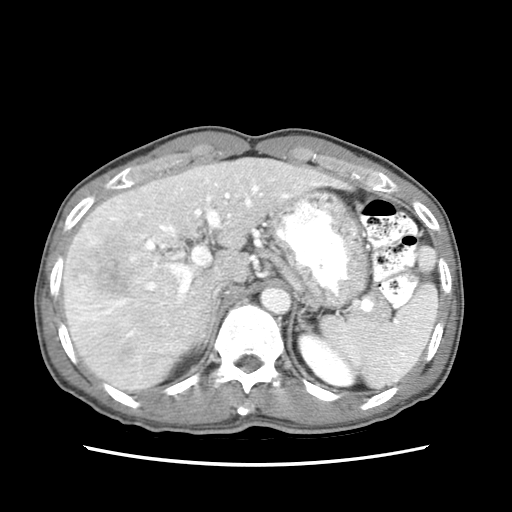
Contrast-enhanced abdominal CT (liver protocol), one axial slice. Position 47 of 79 along the scan axis. Reconstruction kernel STANDARD. Soft-tissue window (W 400 / L 40 HU). 512 × 512 image matrix. Case-level facts recorded for this patient, not image findings: diagnosis: hepatocellular carcinoma (patient treated with transarterial chemoembolisation; whether this scan precedes or follows treatment is not stated here); TNM stage (as recorded): Stage-IIIB; Child-Pugh class: A; tumour differentiation: moderately differentiated; tumour nodularity: multinodular.
Annotated regions visible in this slice (semi-automatically segmented with operator editing):
- liver parenchyma outside the tumour (the mass and vessels are separate outlines, so this box may not span the whole liver): bounding box <62,156,366,391> (left, top, right, bottom; pixels)
- mass: <63,197,143,327>
- liver vessels: <94,168,360,361>